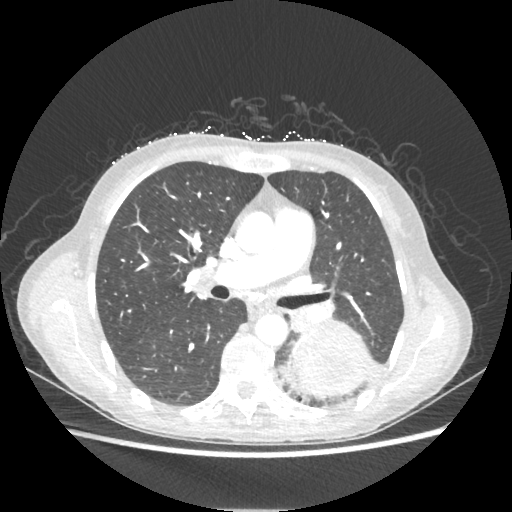
Chest CT, one axial slice. Slice 126 of 221 in the series (ordered by position). 80 kVp. Lung window (W 1500 / L -600 HU). 1.25 mm slice thickness. 512 × 512 image matrix. Female patient, age 53 years. Case-level facts recorded for this patient, not image findings: clinical TNM (as recorded): T3 N0 M0.
Structures marked on this image (bounding box drawn by a radiologist):
- lung tumour (recorded histology: adenocarcinoma): bounding box [x1, y1, x2, y2] px = [292, 323, 370, 397]